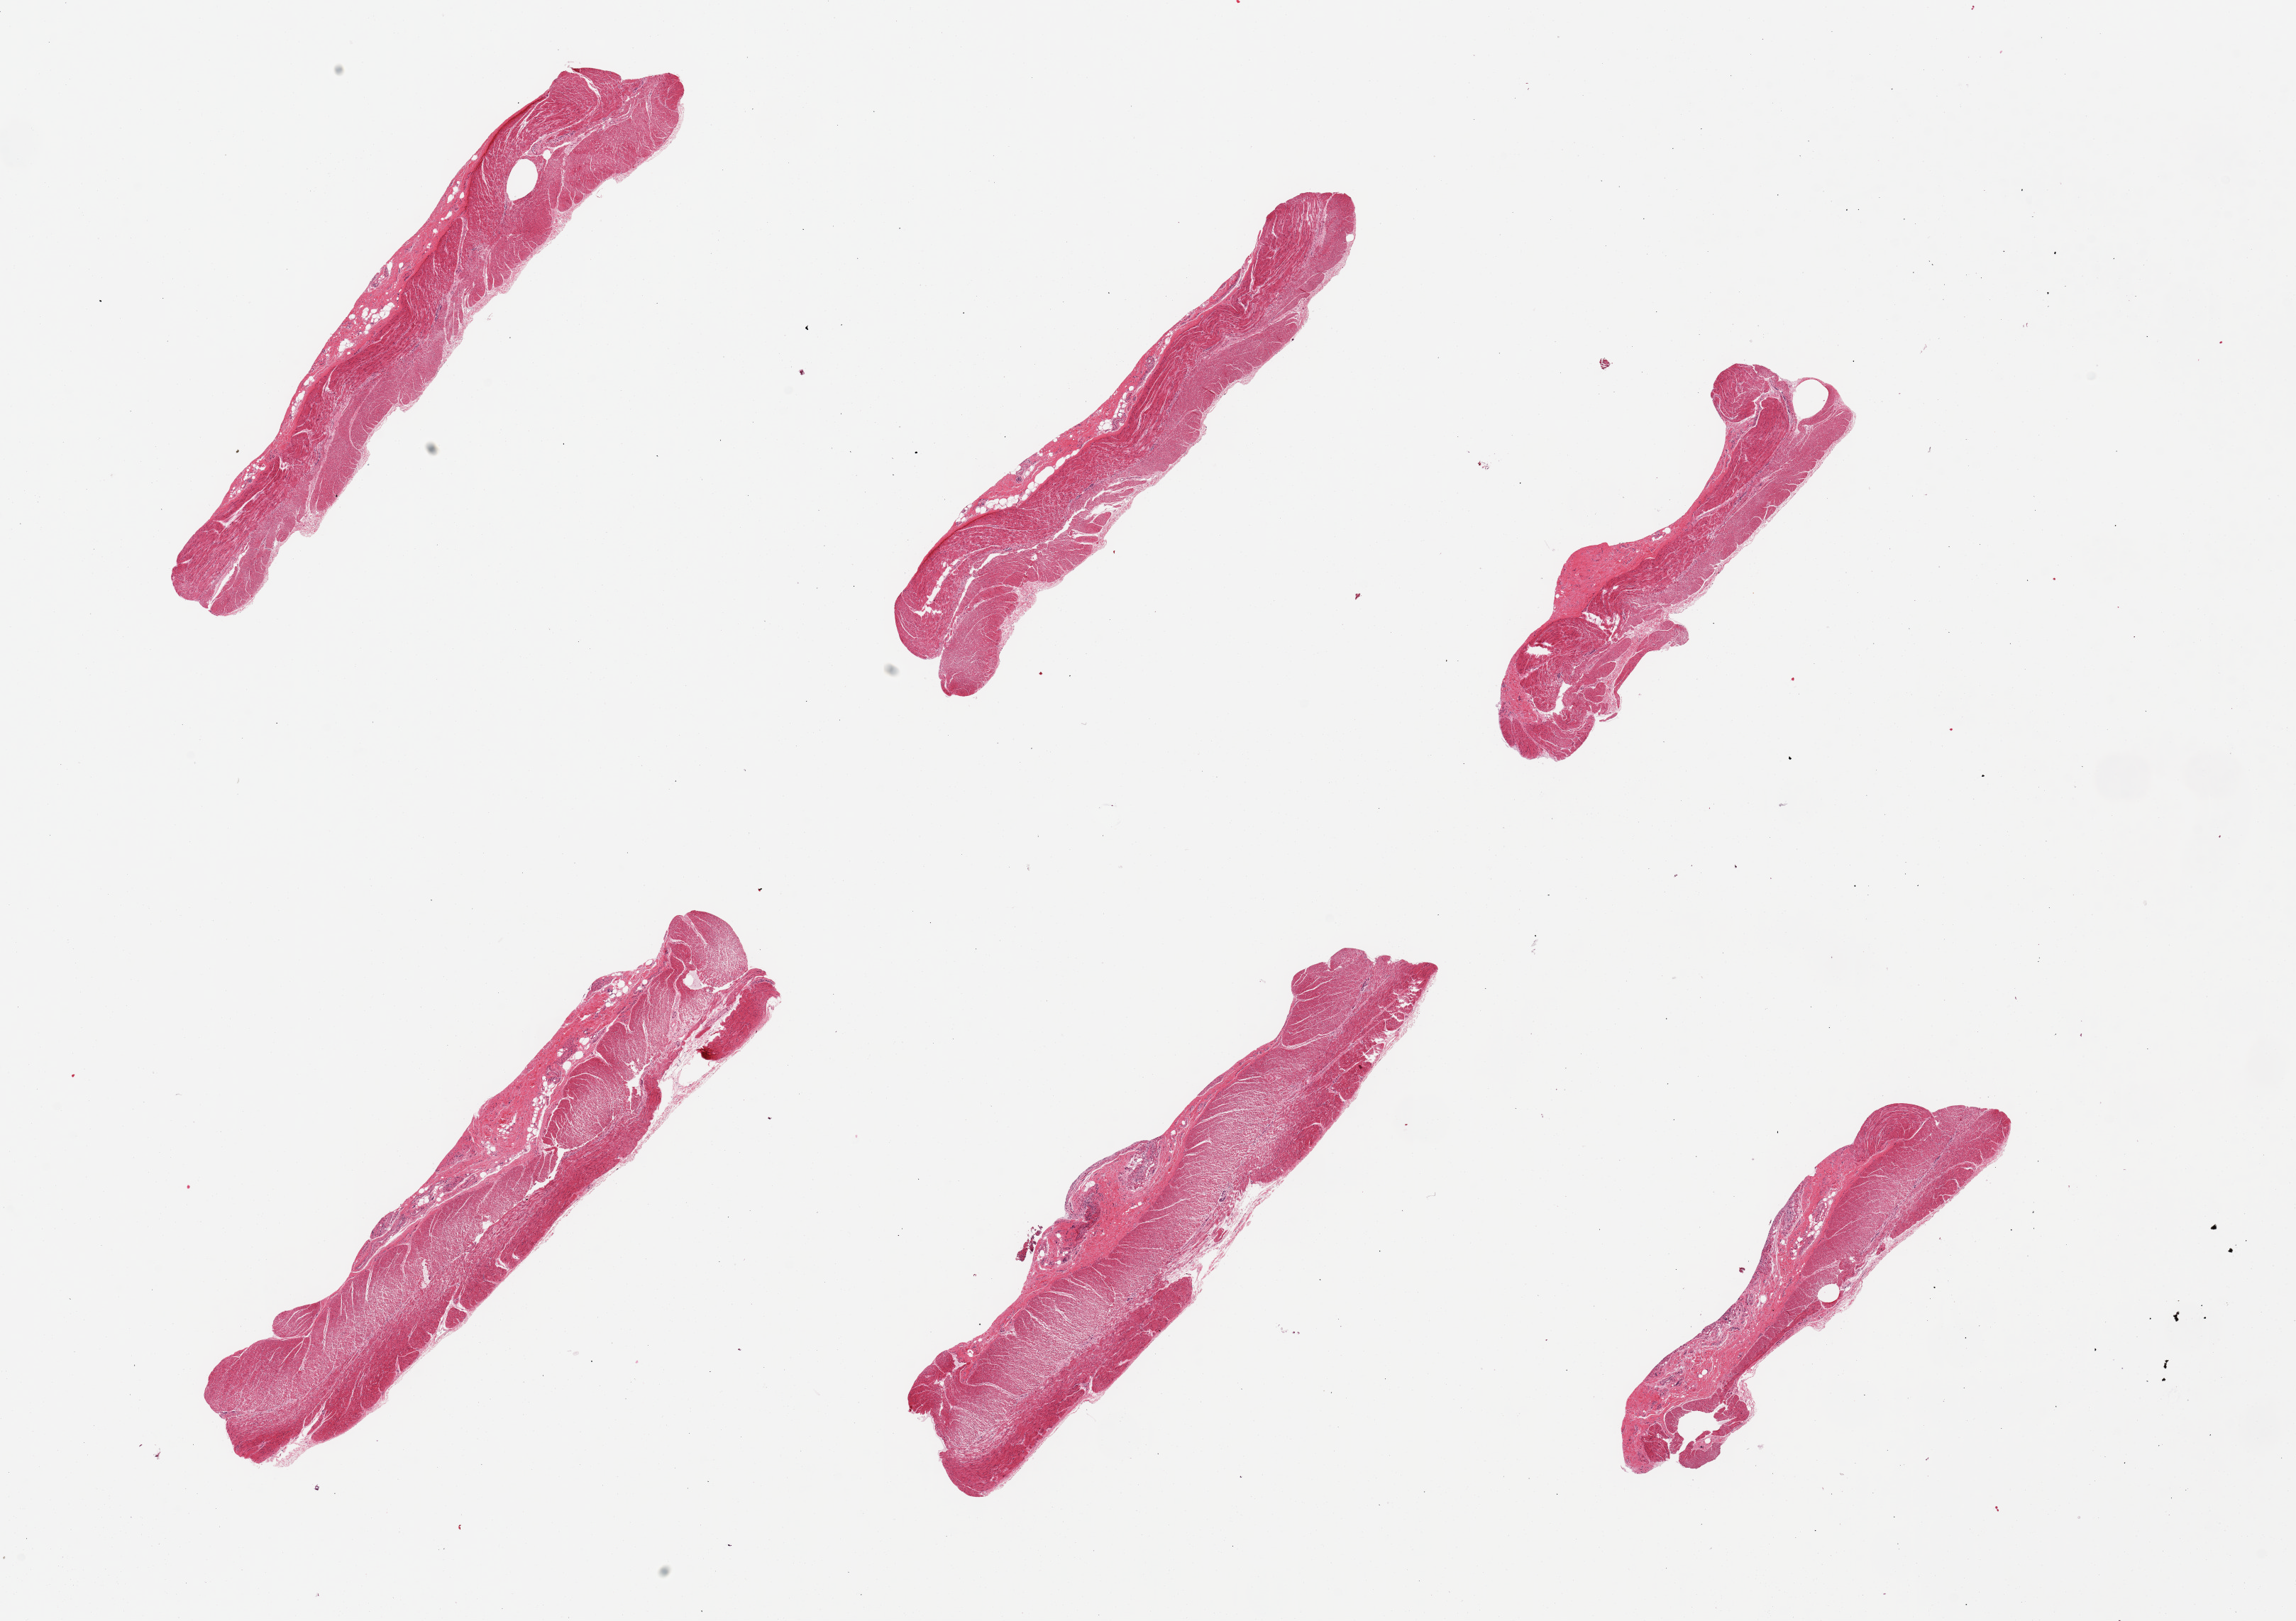
H&E whole-slide image, a low-resolution overview of the entire scanned area, about 25.6 x 18.1 mm. PAXgene-fixed paraffin-embedded (PFPE) section. Sampled site (target tissue): sigmoid colon. Tissue donor sample.
Pathologist's review note for this sample: 6 pieces; well dissected muscle.